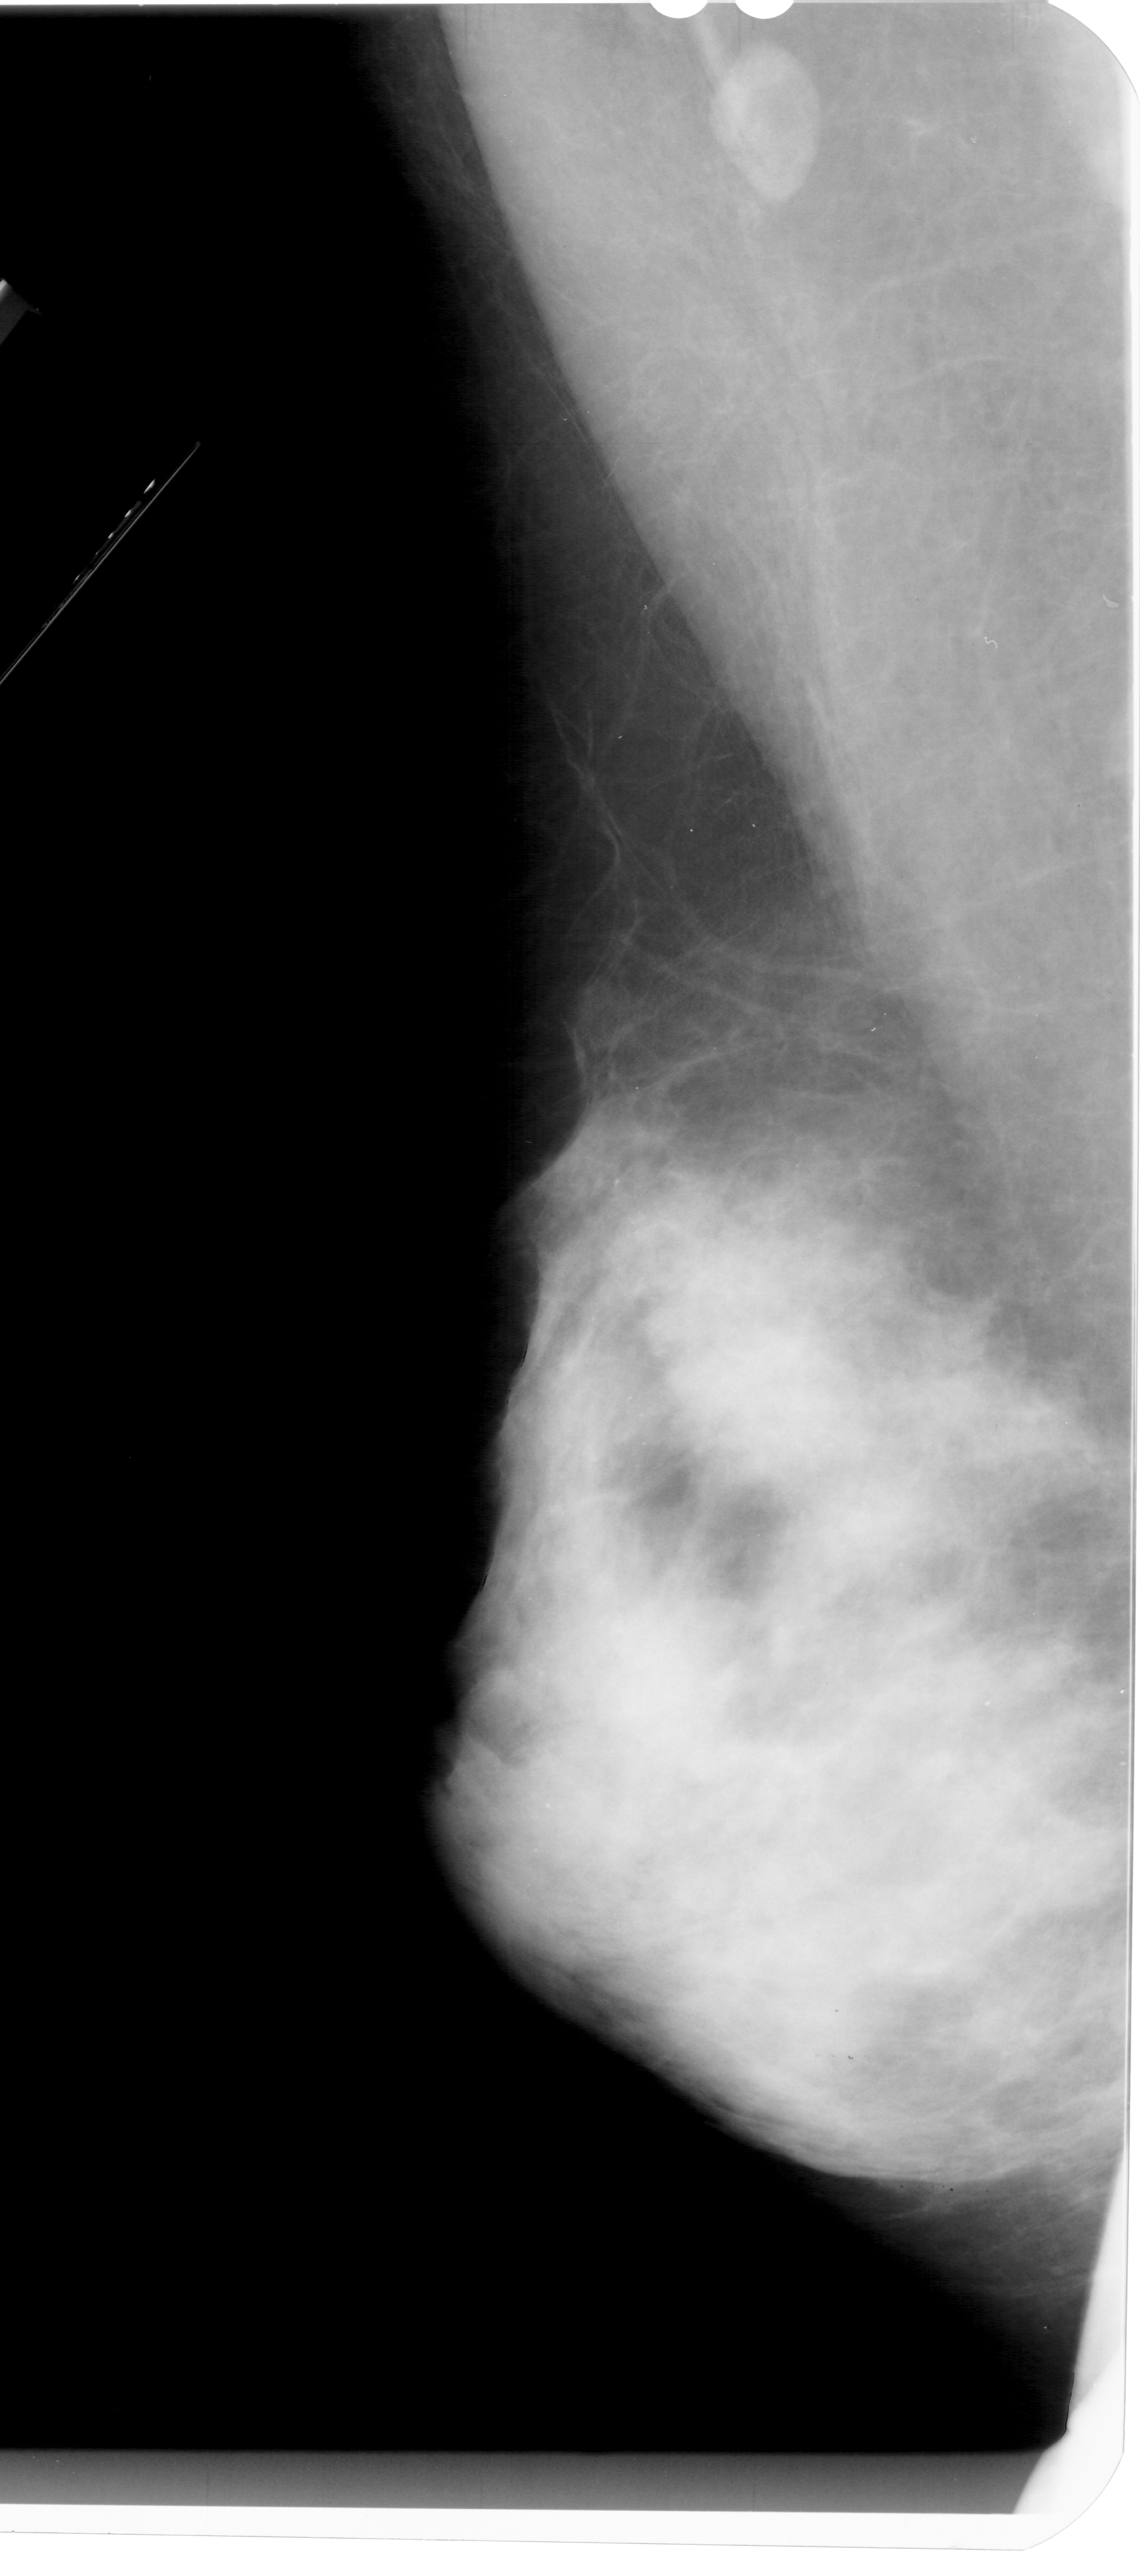
Mammogram (digitized film). Left breast. MLO view. BI-RADS breast density category 4 (scale 1–4). 1140 × 2576 image matrix.
Expert-marked regions of interest on this film, with their recorded descriptors:
- calcifications, morphology punctate, distribution segmental; BI-RADS assessment category 4; pathology (as recorded): malignant: box from (x=568, y=1161) to (x=679, y=1482) px